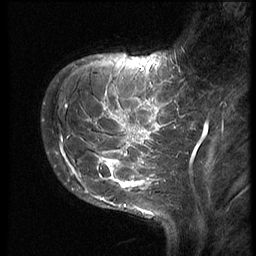
Breast MRI (dynamic contrast-enhanced), one sagittal slice; position 12 of 62 along the scan axis; 3 images stored at this slice position (order not interpretable as contrast timing); 1.5 T; TE 4.2 ms, TR 9 ms; 2.5 mm slice thickness; 256 × 256 image matrix, field of view 180 × 180 mm. Patient: female, 28 years. Case-level facts recorded for this patient, not image findings: setting: breast cancer imaged before/during neoadjuvant chemotherapy.
Outlined on this slice (semi-automatically segmented with operator editing):
- analysis volume of interest (the breast-tissue region the enhancement analysis was run in; not a lesion): box from (x=42, y=75) to (x=192, y=193) px
- tumour enhancement mask (voxels above the 140 % enhancement threshold inside the analysis volume of interest): (x=56, y=102)–(x=192, y=192)